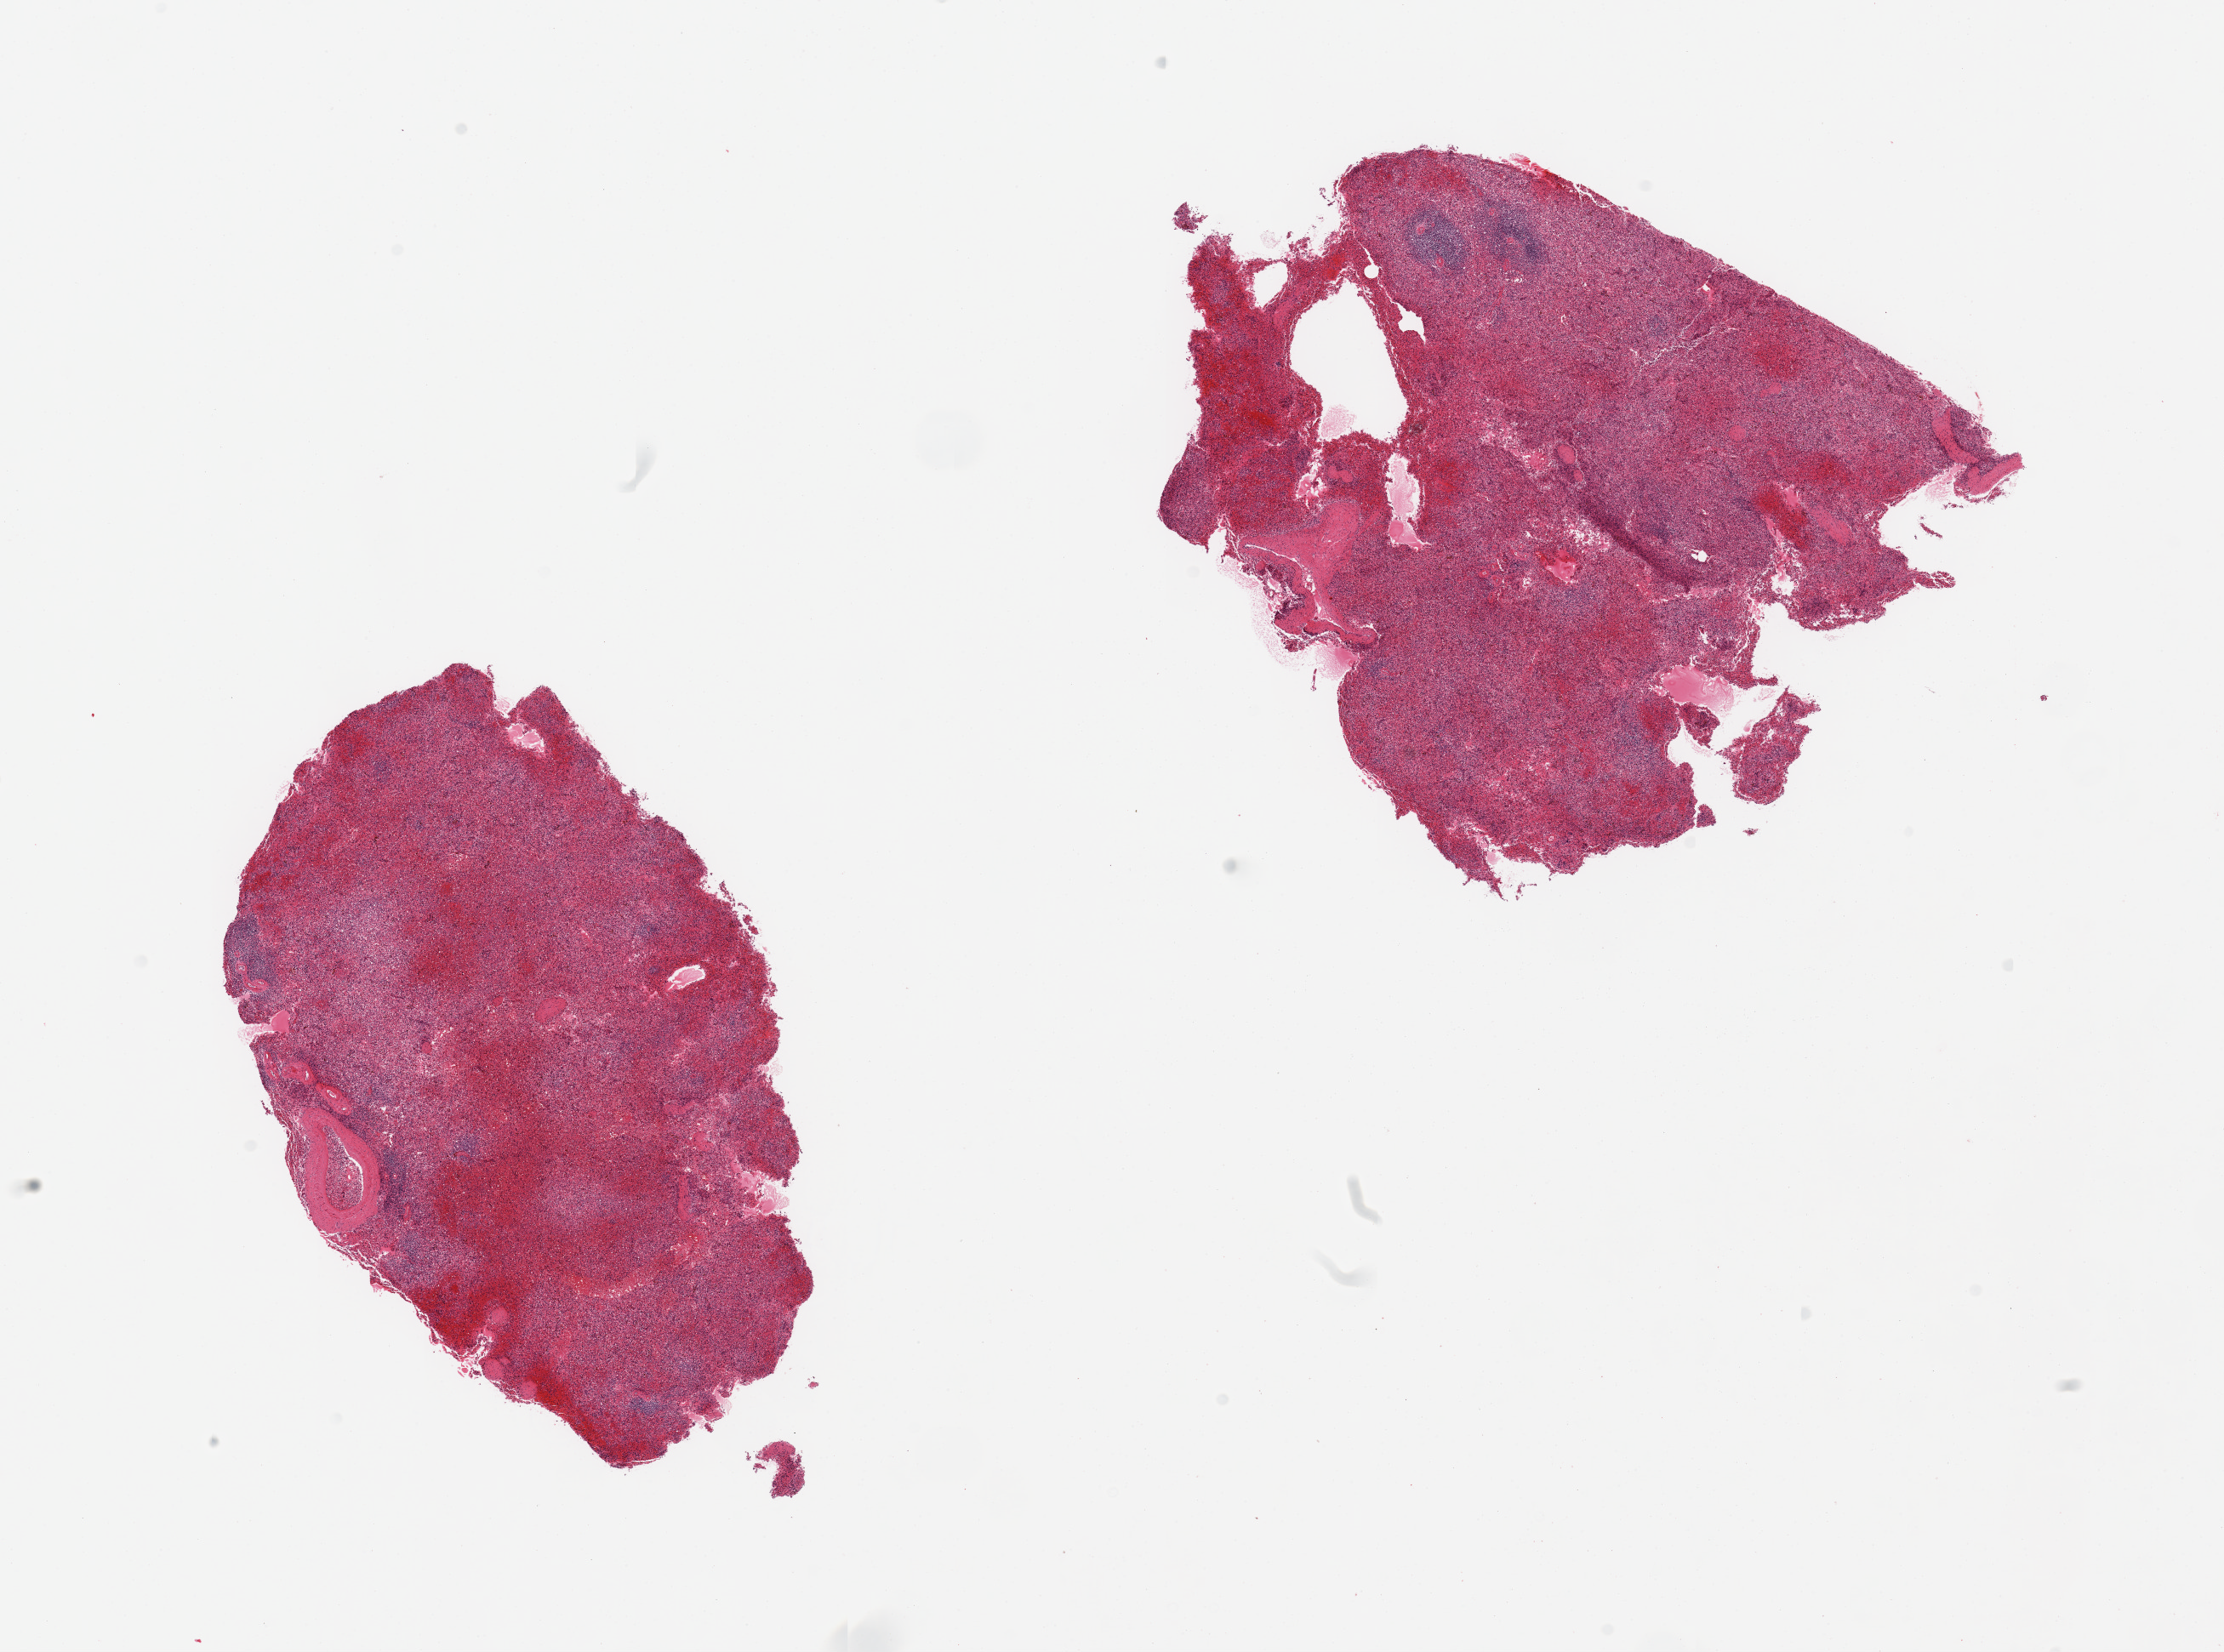
H&E whole-slide image, low-resolution overview of the scanned area, about 20.7 x 15.4 mm (acquisition: 20x scan); PAXgene-fixed paraffin-embedded (PFPE) section; section of spleen (target tissue); tissue donor sample. Donor sex: male.
Reviewer comment on this tissue sample: 2 pieces, marked congestion.